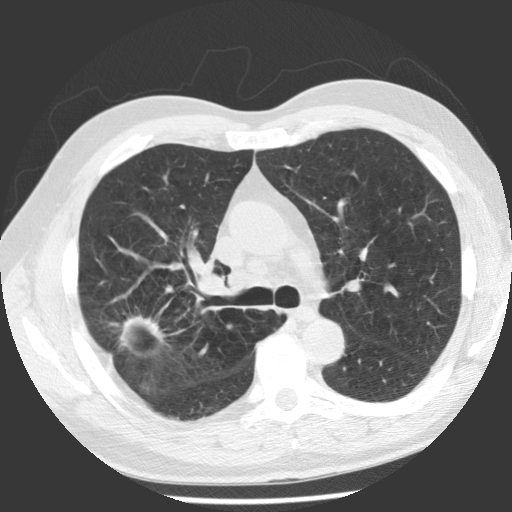
Axial slice from a low-dose chest CT screening exam, baseline screening round, lung window (W 1500 / L -600 HU), 2.5 mm slice thickness, 140 kVp, slice 72 of 112 in the series. Male participant, aged 62 years at enrolment.
Expert-annotated lung lesion, bounding box <103,298,176,367> (left, top, right, bottom; pixels). The screening reader recorded 2 non-calcified nodules or masses ≥4 mm on this exam (right upper lobe, right upper lobe); which of them this box marks is not recorded. Official screen result: positive, change unspecified: nodule(s) >= 4 mm or enlarging nodule(s), mass(es), or other non-specific abnormalities suspicious for lung cancer. Participant outcome: lung cancer diagnosed 71 days after this screen — adenocarcinoma, NOS, right upper lobe, poorly differentiated (G3), stage IV (AJCC 6th edition), 30 mm at pathology.